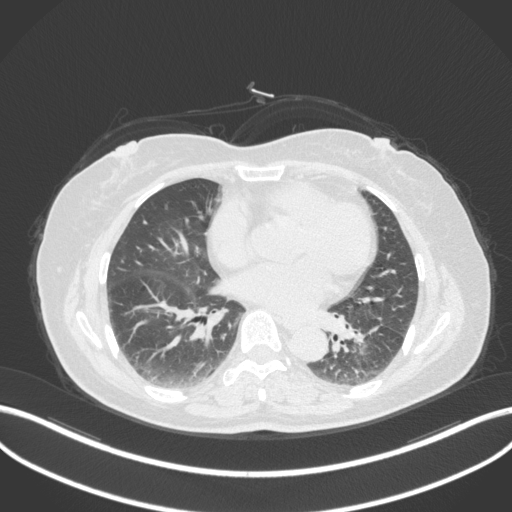
Chest CT, one axial slice; position 166 of 307 along the scan axis; 120 kVp; lung window (W 1500 / L -600 HU); 1 mm slice thickness; 512 × 512 image matrix. Patient: female, 59 years. From the clinical record (not read from this slice): clinical TNM (as recorded): T2a N0 M0.
Annotated regions visible in this slice (rectangle marked by the reading radiologist):
- lung tumour (recorded histology: adenocarcinoma): bounding box <354,317,385,349> (left, top, right, bottom; pixels)